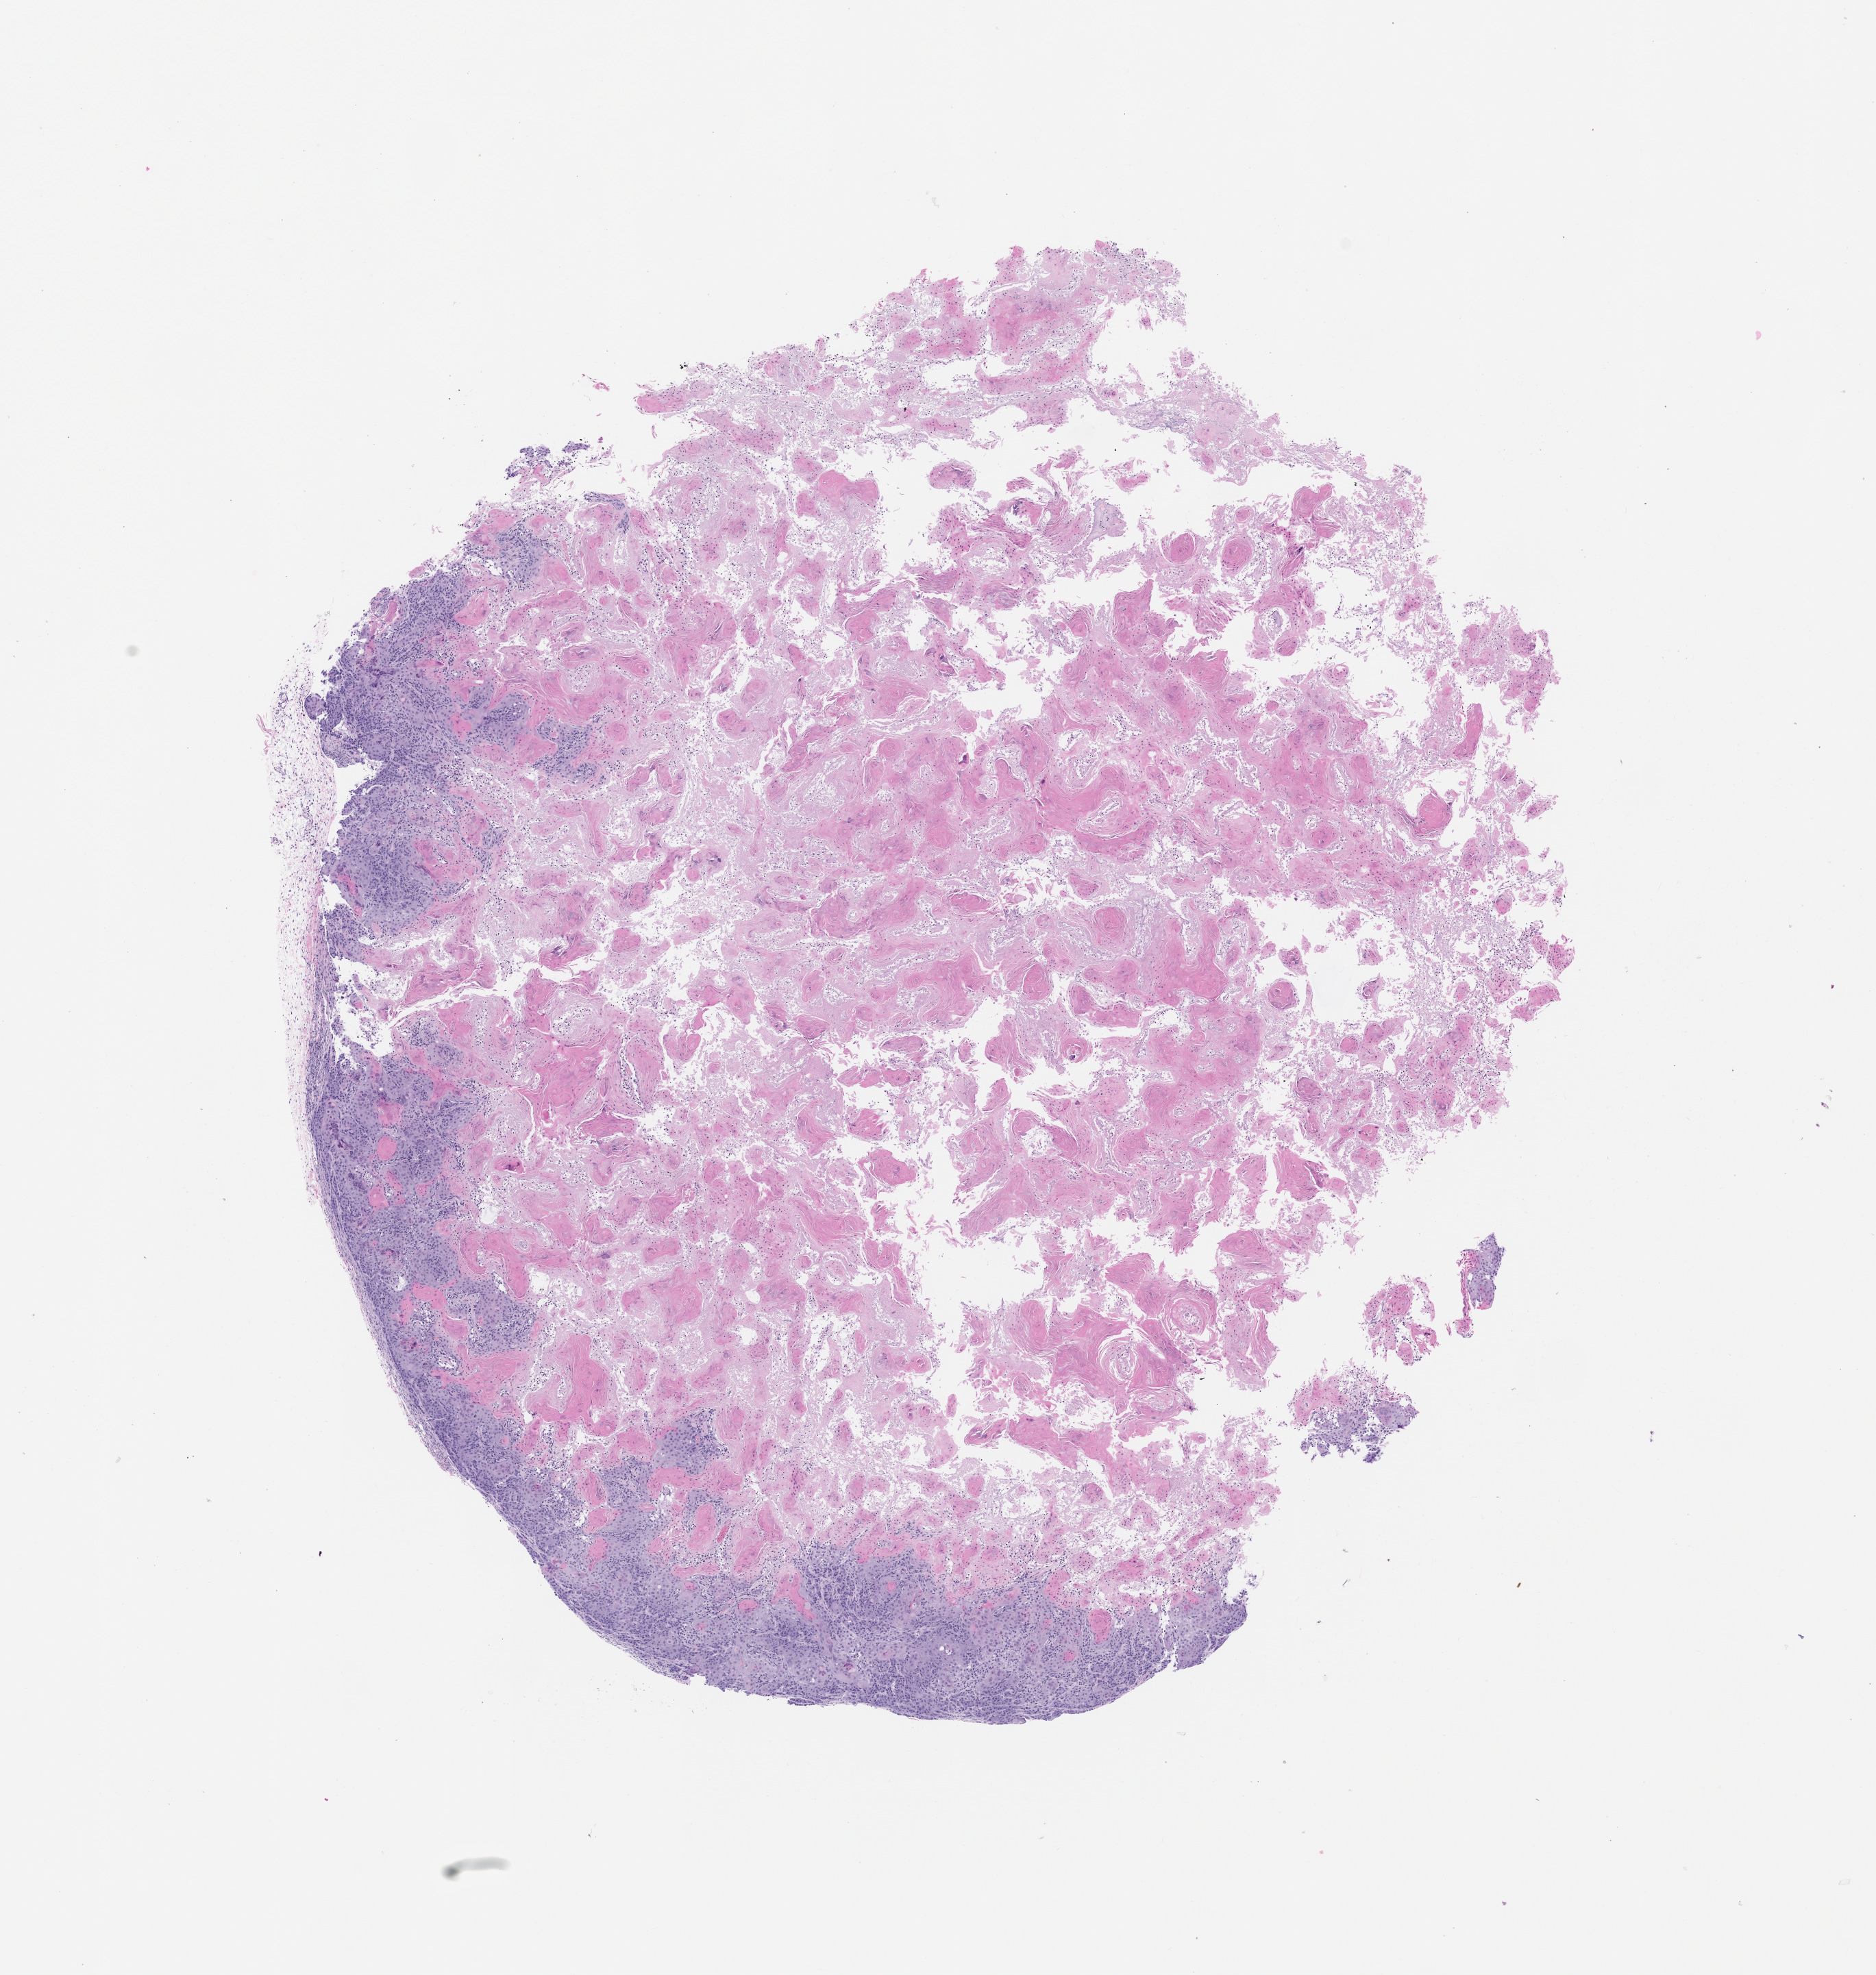
H&E whole-slide image of a patient-derived xenograft (PDX) tumor grown in a mouse, passage 0, low-resolution overview of the scanned area, about 11.0 x 11.5 mm, formalin-fixed, paraffin-embedded (FFPE) tissue, originating tumor site category: oral soft tissue.
Originating patient diagnosis: Head and Neck Squamous Cell Carcinoma.